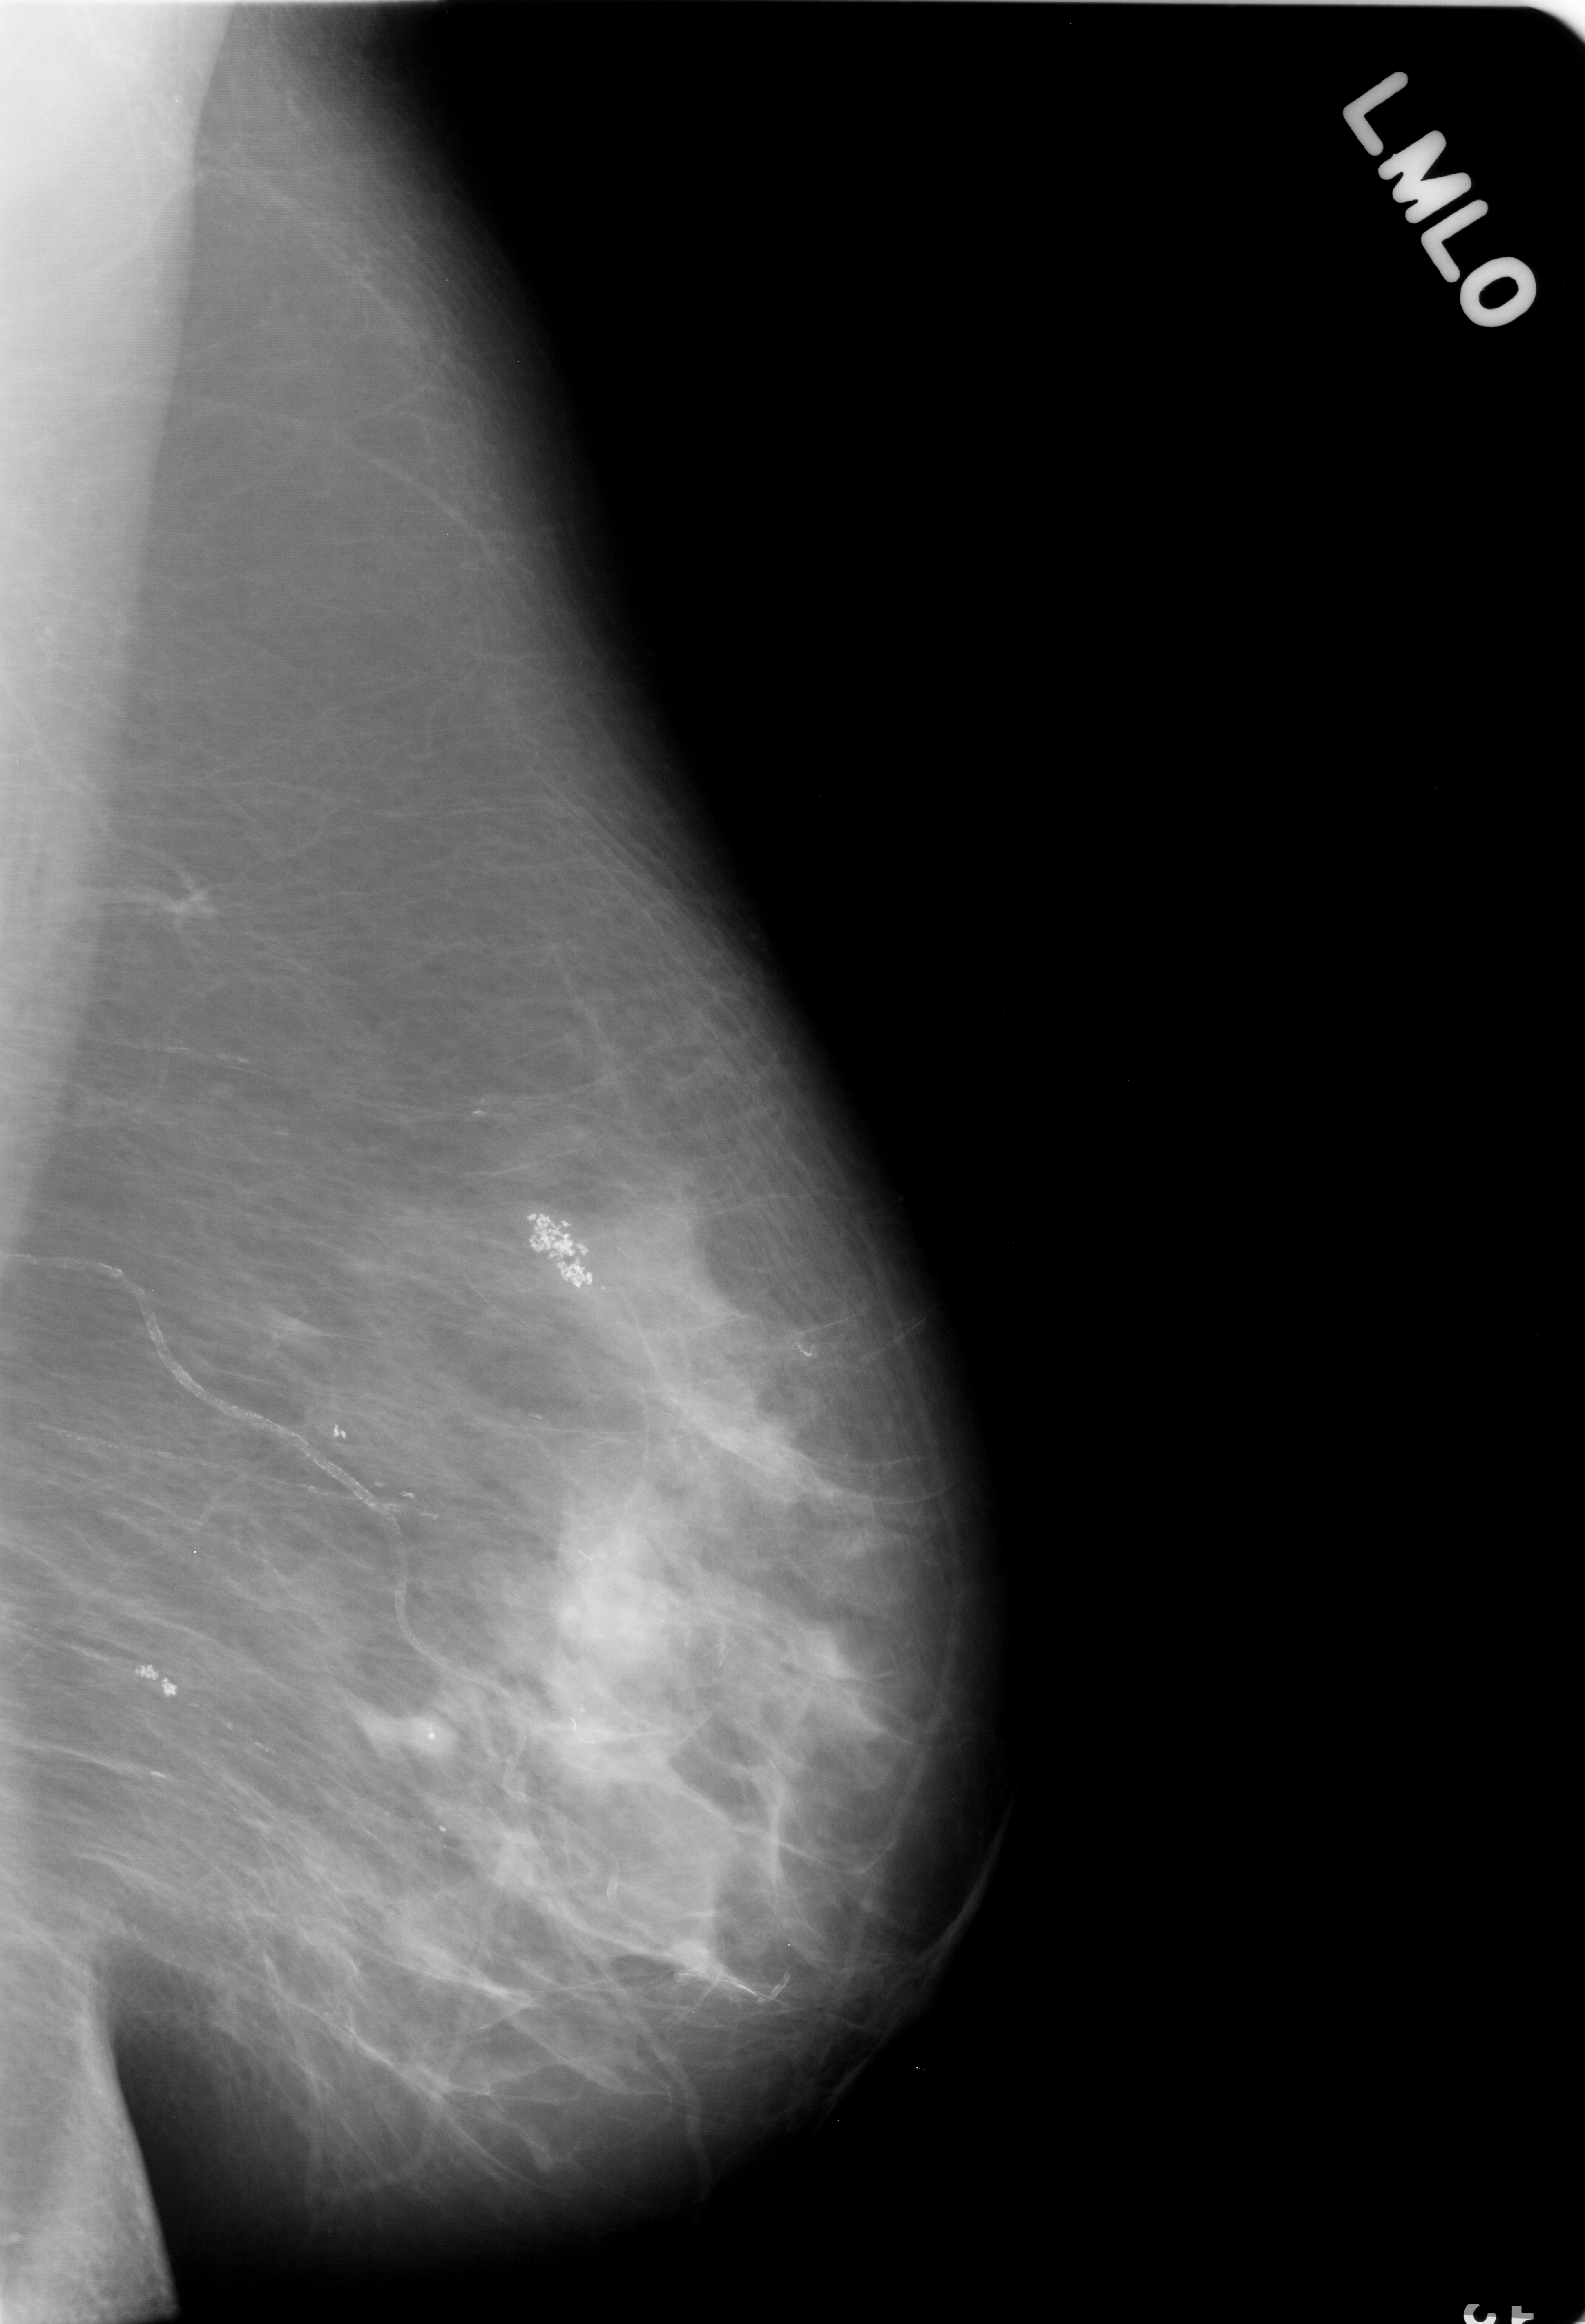
Mammogram (digitized film); left breast; mediolateral oblique (MLO) view; breast composition: scattered fibroglandular densities (BI-RADS density category 2 of 4); 1585 × 2324 image matrix.
Expert-marked regions of interest on this film, with their recorded descriptors:
- Finding 1 of 2: calcifications, morphology pleomorphic, distribution clustered; BI-RADS assessment category 4; pathology (as recorded): benign: box from (x=91, y=1617) to (x=236, y=1763) px
- Finding 2 of 2: calcifications, morphology pleomorphic, distribution clustered; BI-RADS assessment category 4; subtlety rating 5 on a 1 (subtle) to 5 (obvious) scale; pathology (as recorded): benign: (x=454, y=1121)–(x=661, y=1344)